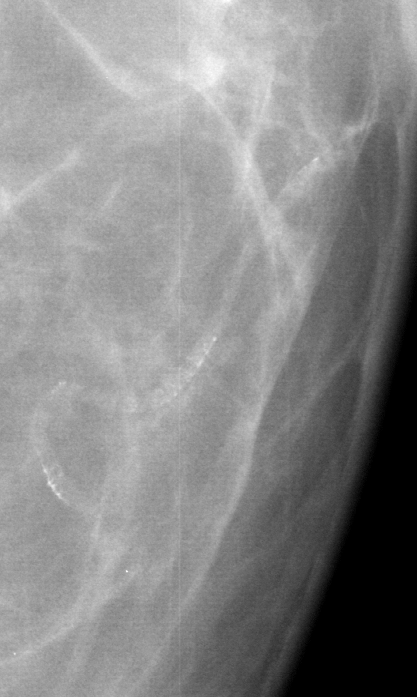
Crop from a digitized film mammogram around one marked abnormality, left breast, CC view.
Calcifications, morphology vascular; BI-RADS assessment category 2; subtlety rating 5 on a 1 (subtle) to 5 (obvious) scale; benign without callback (not worked up further).